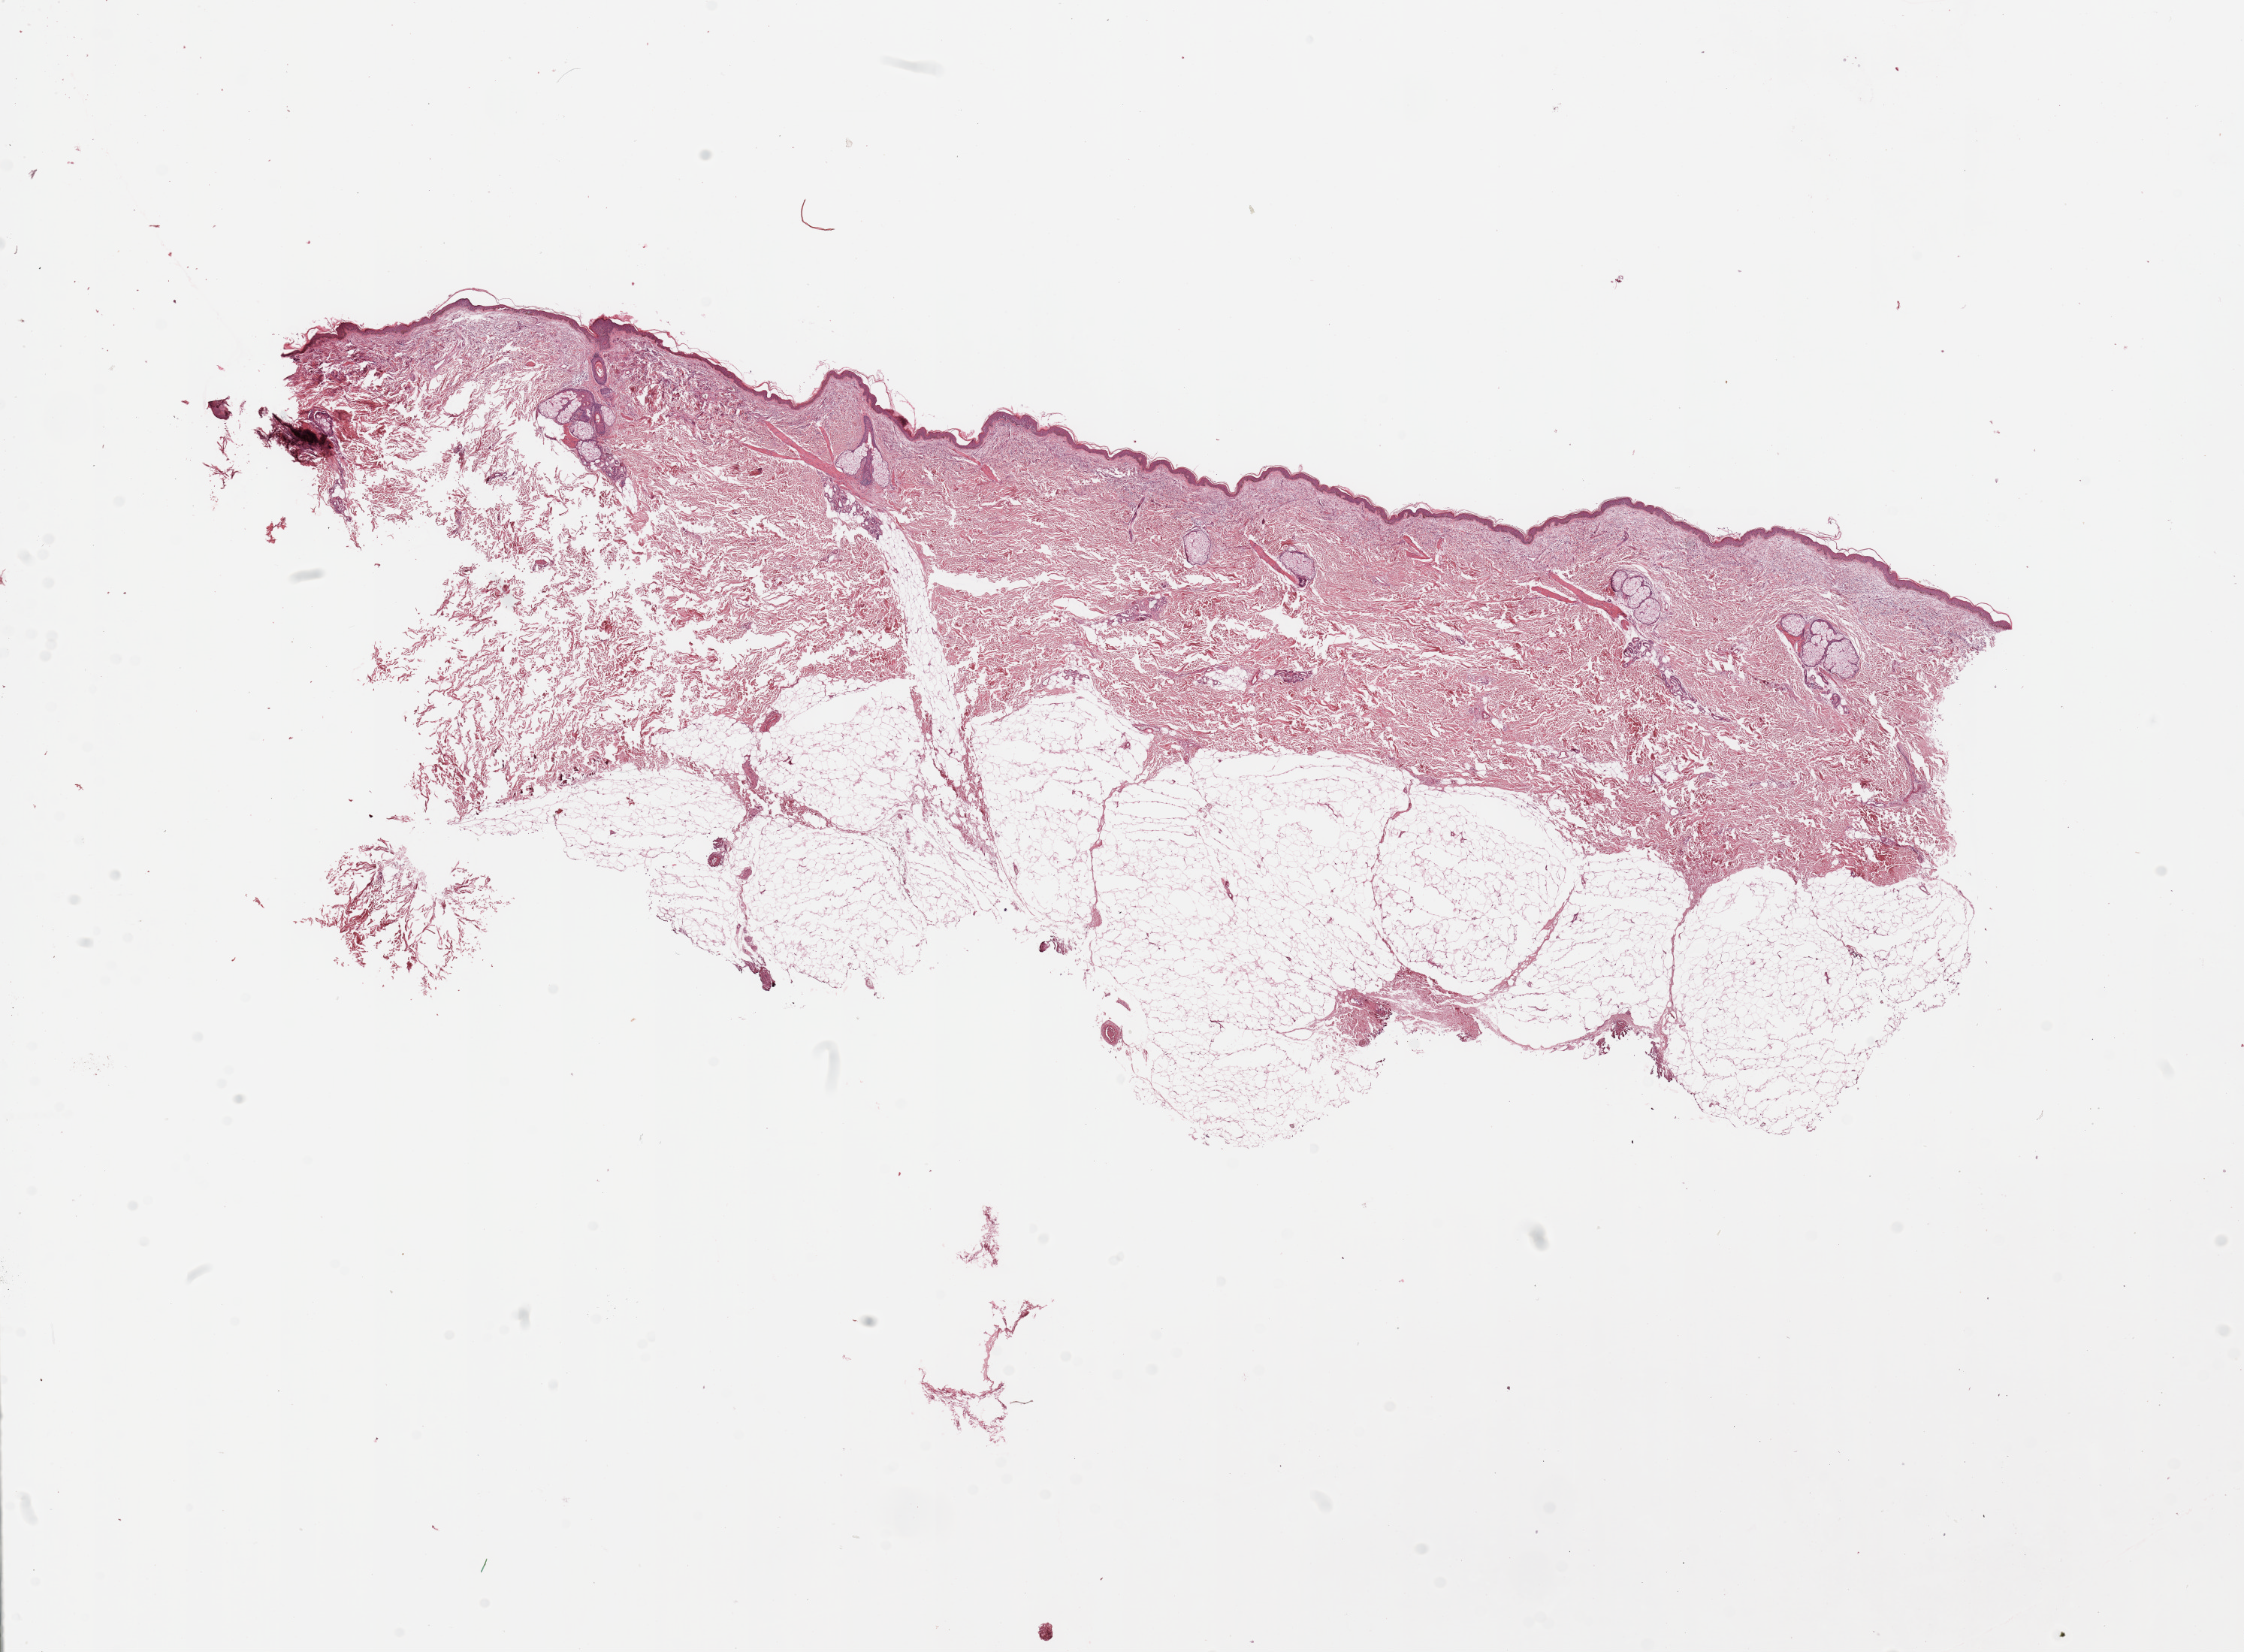
H&E-stained whole-slide image, low-resolution overview of the scanned area, about 23.6 x 17.4 mm; normal (non-tumour) tissue sample, sampled site: skin. Patient: male, age 59 years.
This section: normal (non-tumour) tissue from the same patient. Patient diagnosis: Malignant melanoma, NOS.